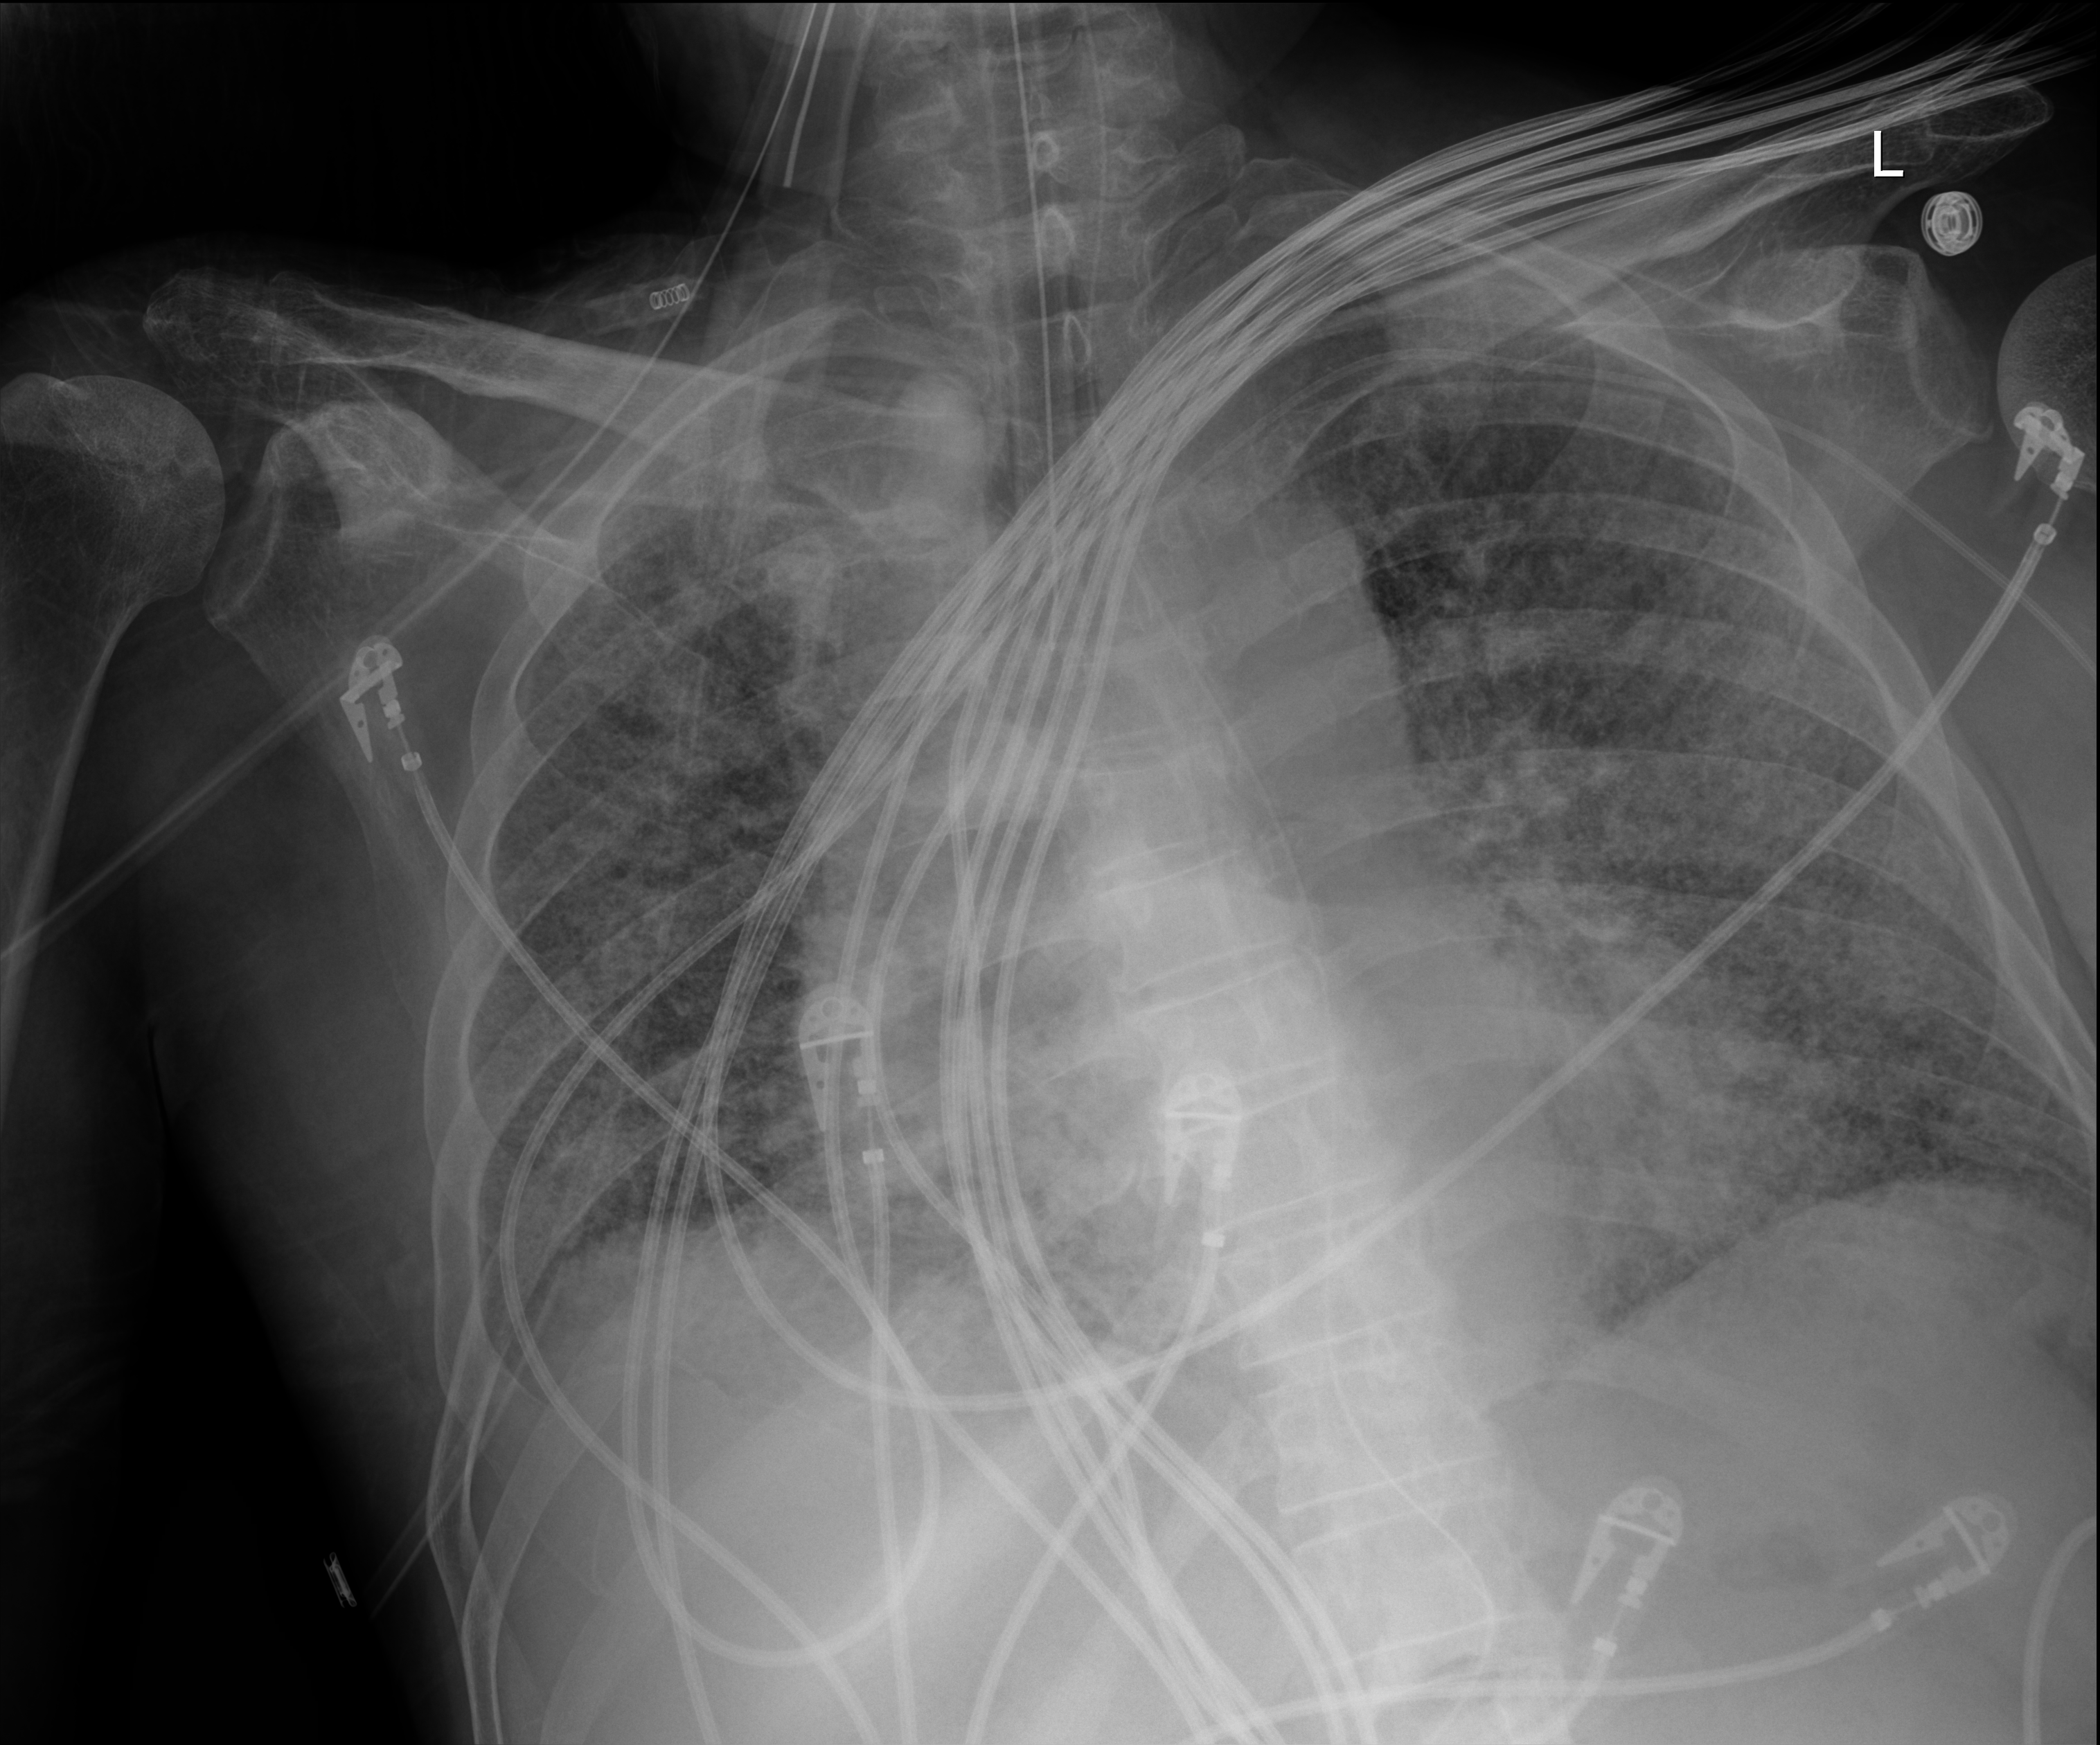
Chest radiograph (digital radiography), anteroposterior (AP) projection. Male patient hospitalised with COVID-19, age 60–74 years.
From the hospital-stay record, not from the radiograph (when in the stay this image was taken is not recorded):
- length of hospital stay: 54 days